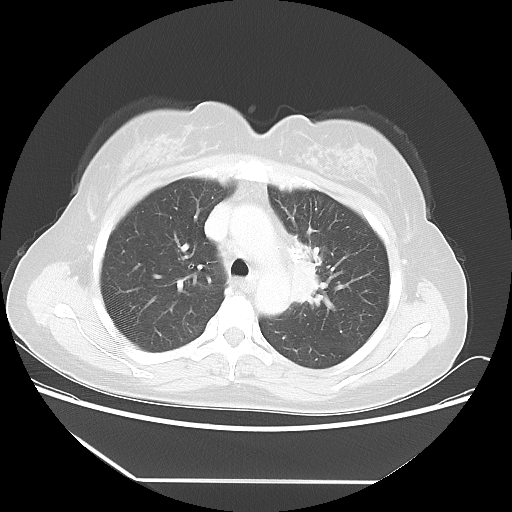
Chest CT, one axial slice. Slice 37 of 52 in the series (ordered by position). Reconstruction kernel LUNG. Lung window (W 1500 / L -600 HU). 512 × 512 image matrix, field of view 390 × 390 mm. Patient: female, 50 years. Case-level facts recorded for this patient, not image findings: clinical TNM (as recorded): T2 N3 M0.
Structures marked on this image (bounding box drawn by a radiologist):
- lung tumour (recorded histology: adenocarcinoma): bounding box <282,236,331,317> (left, top, right, bottom; pixels)